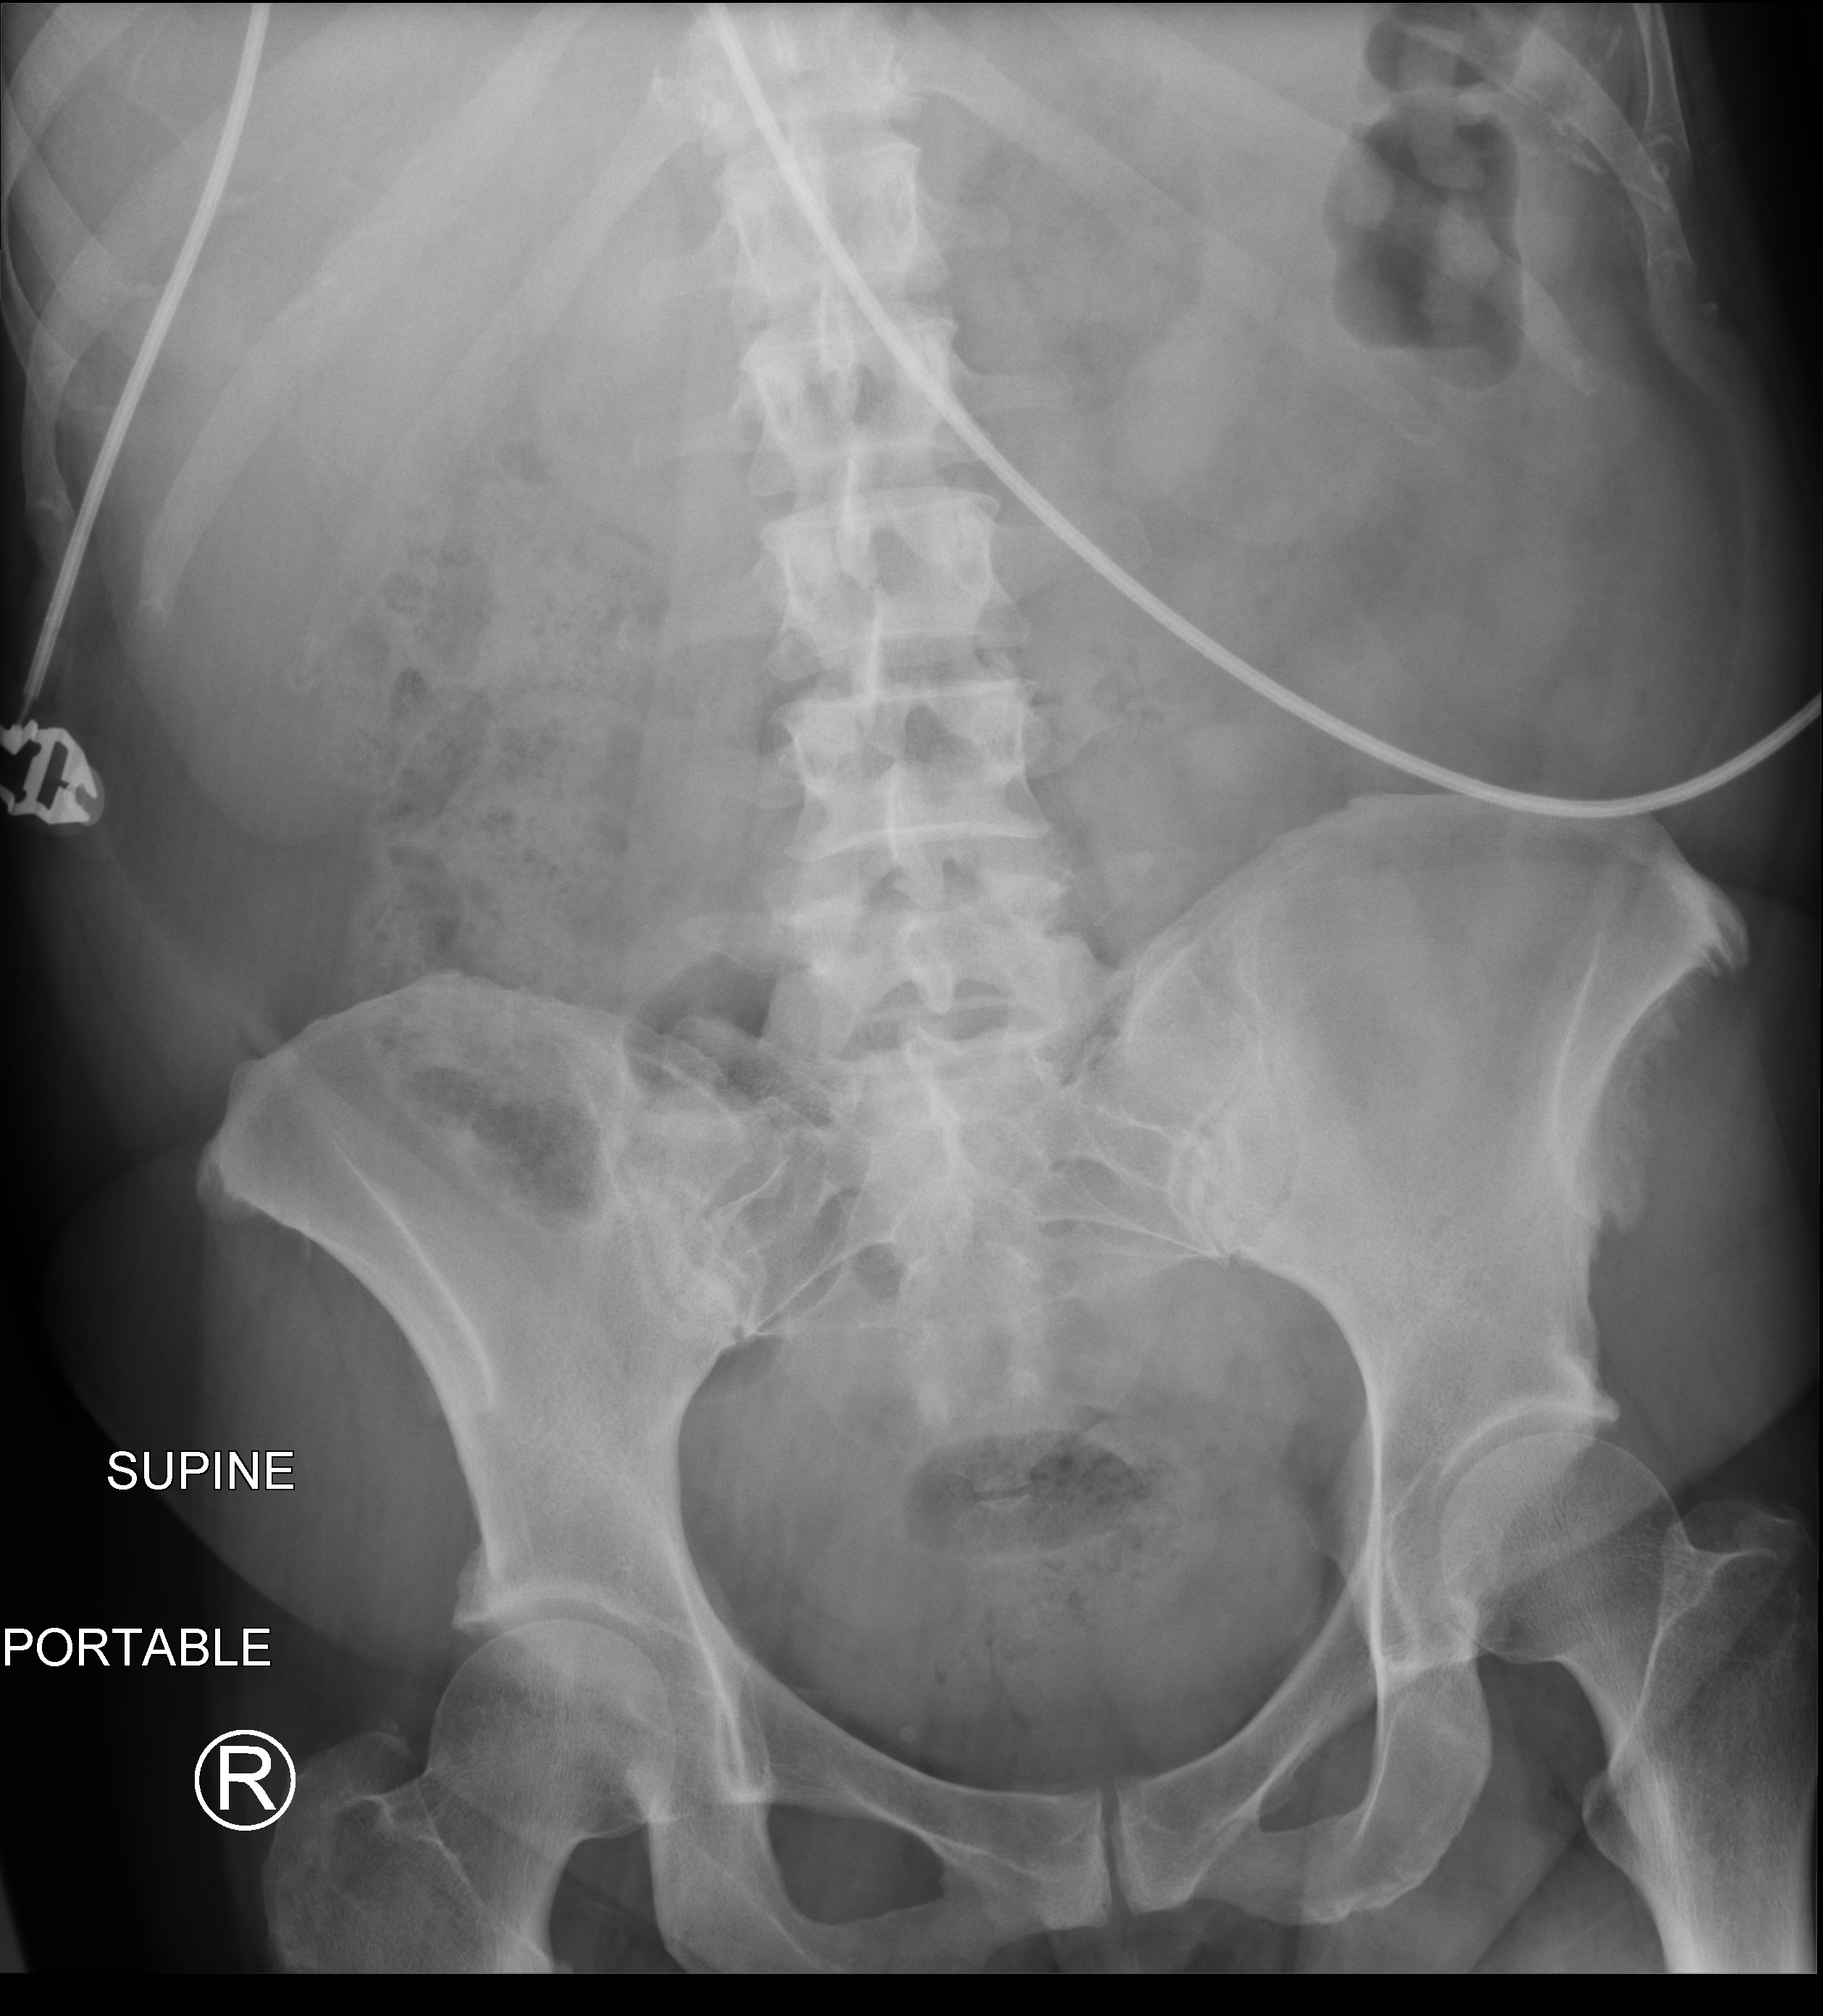
Portable abdomen radiograph; anteroposterior (AP) projection. Female patient hospitalised with COVID-19, age 18–59 years.
From the hospital-stay record, not from the radiograph (when in the stay this image was taken is not recorded): admitted to intensive care during this hospital stay: no; COPD (admission record): no; mechanically ventilated during this hospital stay: no.